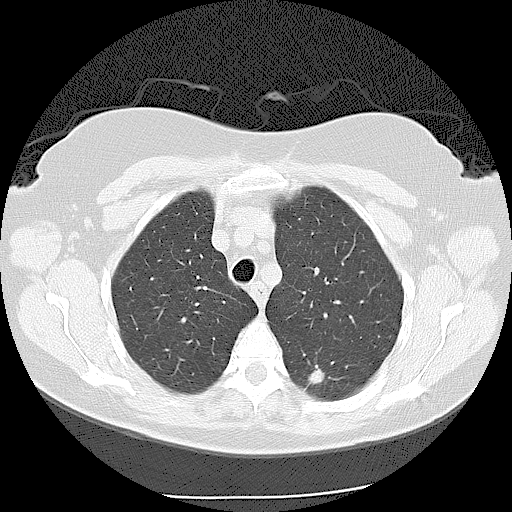
Chest CT (low-dose screening protocol), one axial image. Second screening round (one year after baseline). Lung window (W 1500 / L -600 HU). Lung (sharp) reconstruction kernel (LUNG). Slice 29 of 116 in the series. 512 × 512 image matrix. Female, age 56 years at enrolment.
Expert-annotated lung lesion, box from (x=290, y=347) to (x=350, y=405) px. Screening reader's record for this exam (one nodule recorded; not confirmed to be the boxed lesion): non-calcified nodule or mass ≥4 mm, left lower lobe, 9 × 9 mm, spiculated (stellate) margins, soft tissue attenuation, pre-existing on the prior screen: yes; interval growth: yes. Participant outcome: lung cancer diagnosed 173 days after this screen — adenocarcinoma, NOS, left lower lobe, moderately differentiated (G2), stage IIA (AJCC 6th edition), 15 mm at pathology.